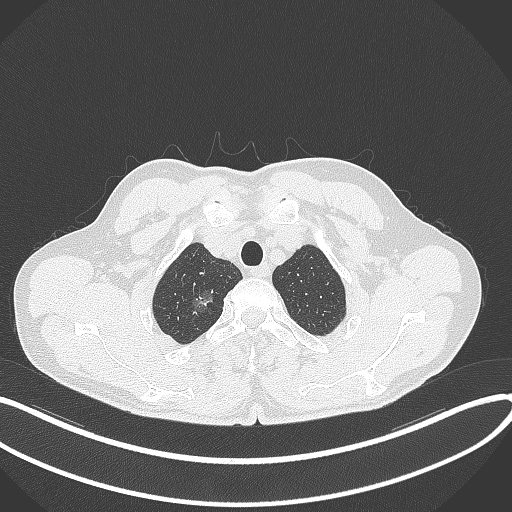
Chest CT, one axial slice; slice 341 of 407 in the series (ordered by position); reconstruction kernel B70f; lung window (W 1500 / L -600 HU); 1 mm slice thickness; 512 × 512 image matrix, field of view 400 × 400 mm. Patient: male, 58 years. From the clinical record (not read from this slice): clinical TNM (as recorded): T1c N0 M0.
Annotated regions visible in this slice (rectangle marked by the reading radiologist):
- lung tumour (recorded histology: adenocarcinoma): bounding box <184,279,216,310> (left, top, right, bottom; pixels)